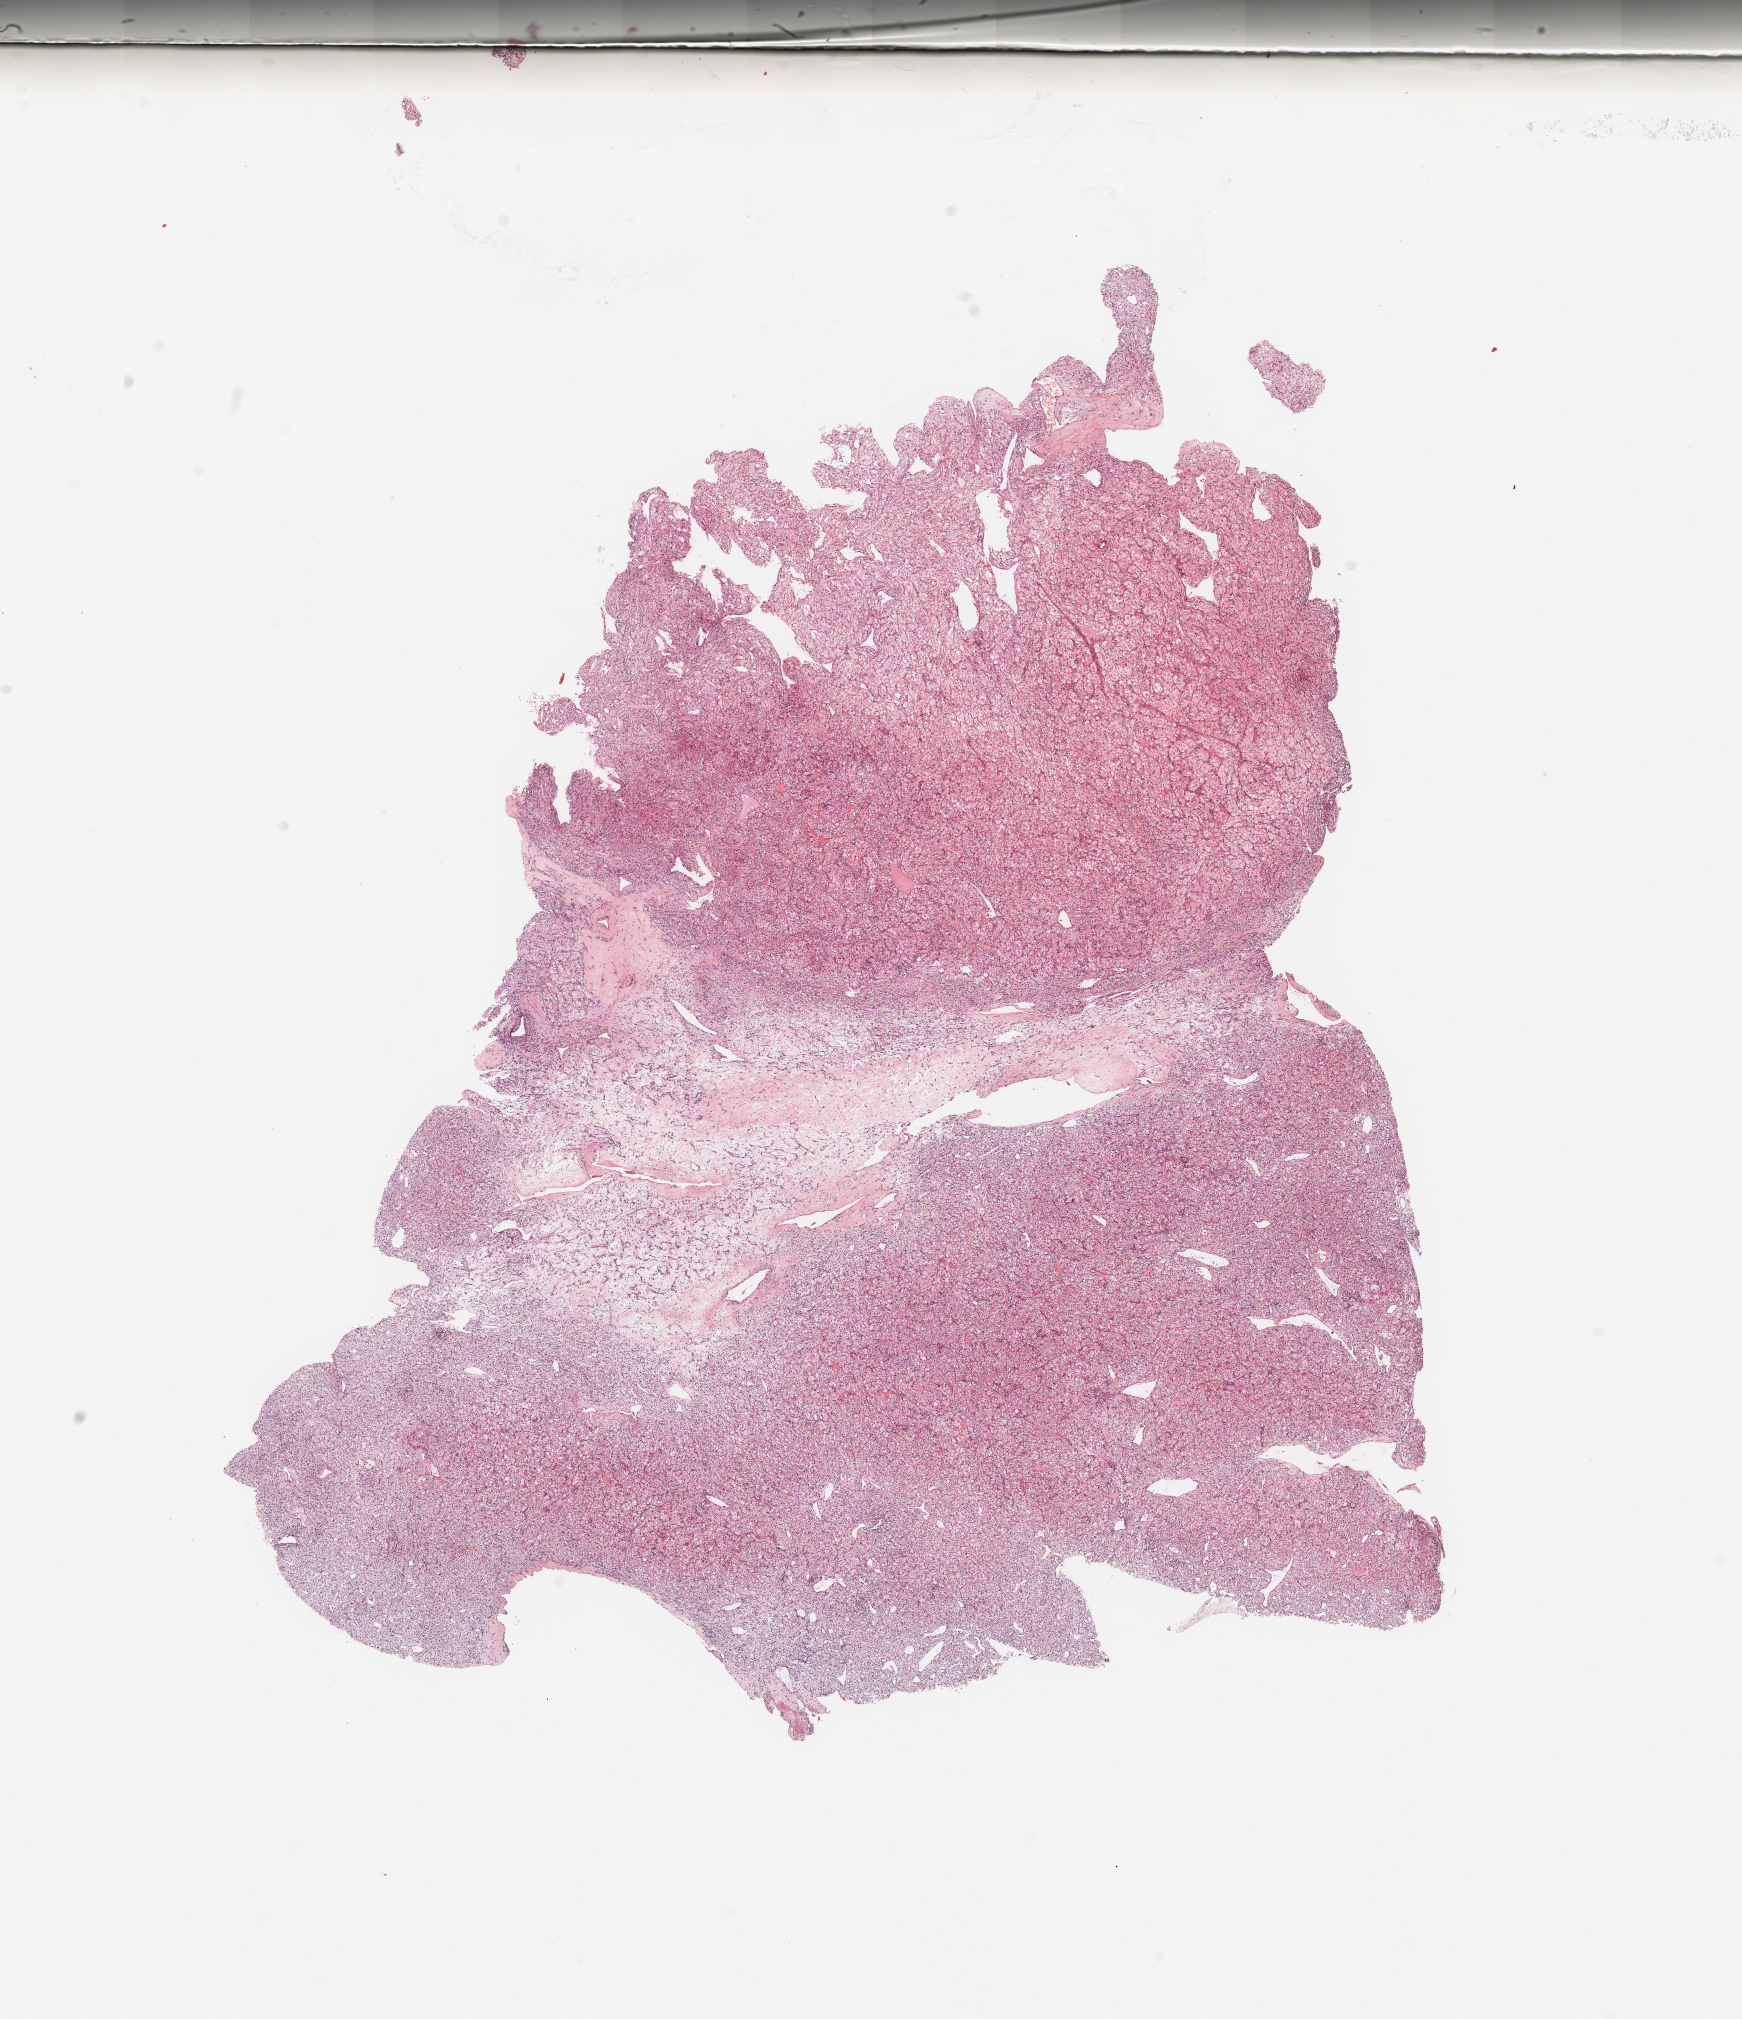
Hematoxylin and eosin (H&E) stained whole-slide image — low-resolution overview of the scanned area, about 13.8 x 16.0 mm; tumour tissue sample, sampled site: kidney. 51-year-old male patient. Histologic grade: G2 (moderately differentiated). Composition of this section per pathologist review: tumour nuclei 90%, necrosis 2%.
AJCC pathologic stage: I. Diagnosis: Renal cell carcinoma, NOS.